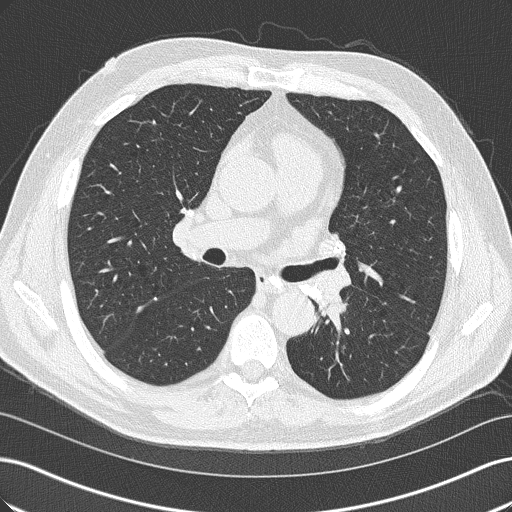
Chest CT (low-dose screening protocol), one axial image; baseline screening round; lung window (W 1500 / L -600 HU); 2 mm slice thickness; 120 kVp; slice 75 of 152 in the series. Male, age 57 years at enrolment.
Expert reader's lesion annotation, bounding box (x1, y1, x2, y2) in pixels: (303, 282, 364, 341). No non-calcified nodule or mass ≥4 mm was recorded by the screening reader at this exam. Official screen result: negative screen, minor abnormalities not suspicious for lung cancer. Lung cancer was diagnosed 363 days after this screen: squamous cell carcinoma, NOS, left lower lobe, moderately differentiated (G2), stage IIIB (AJCC 6th edition), 38 mm at pathology.